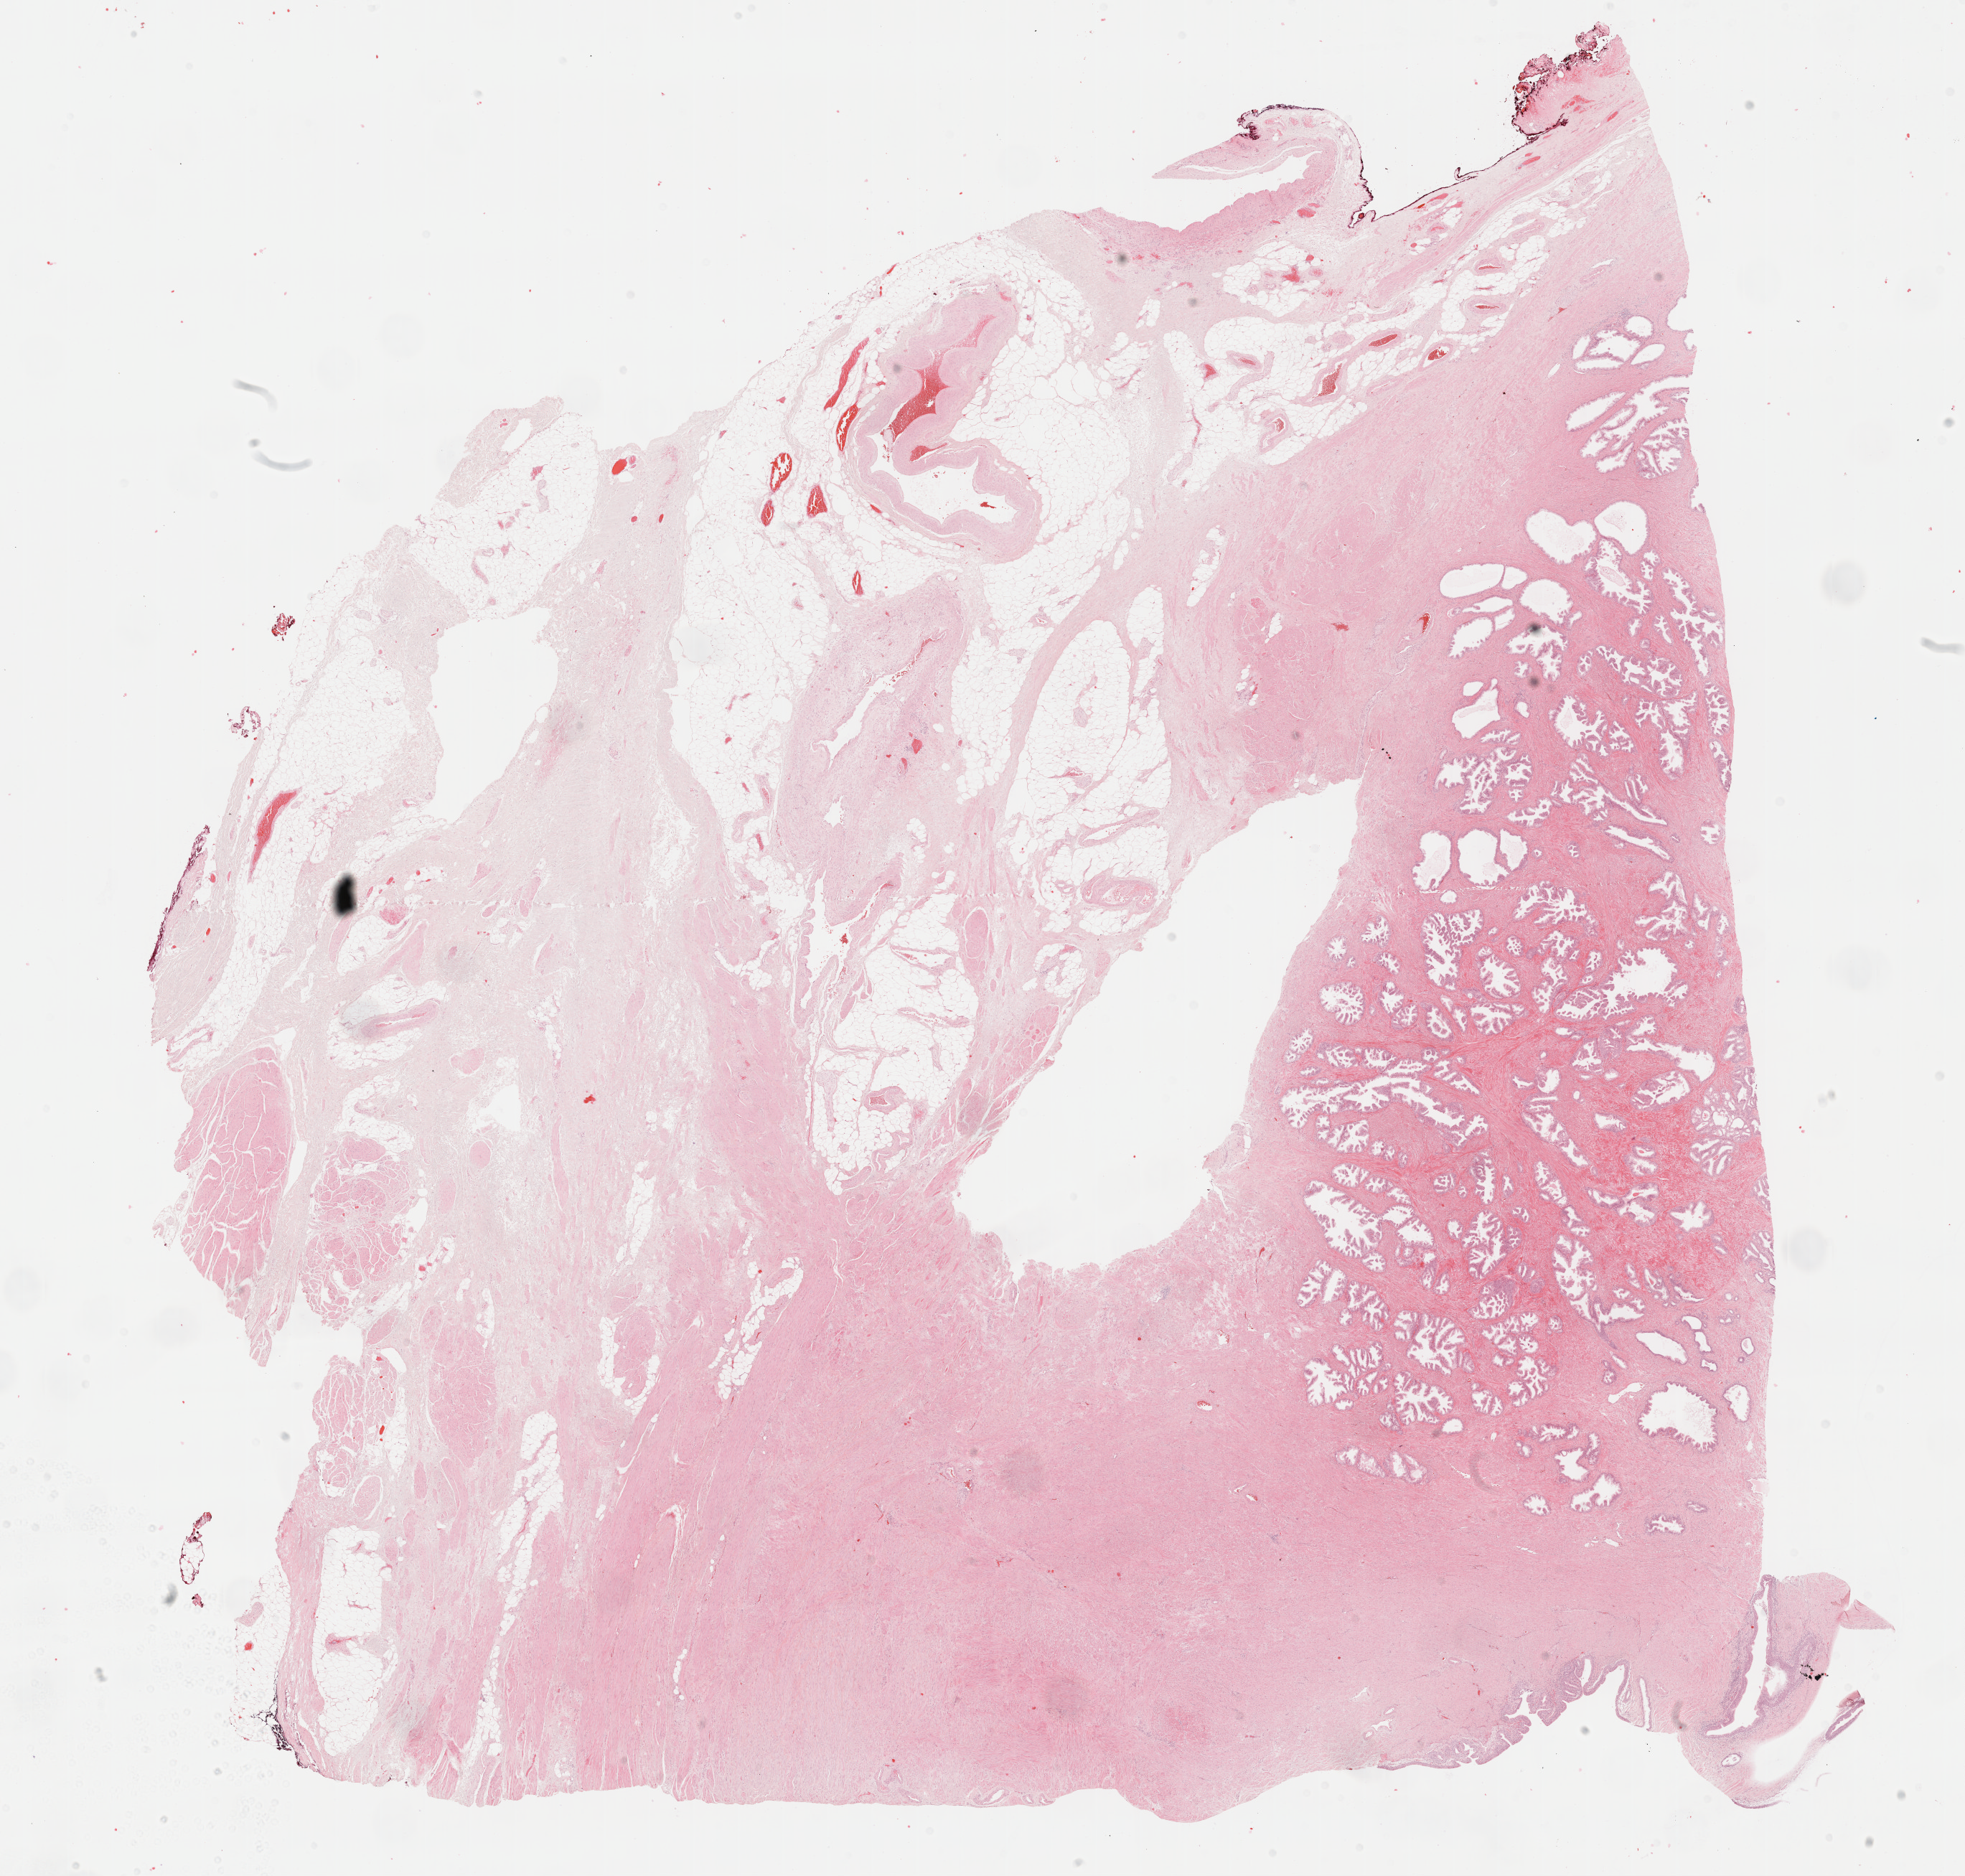
Digitized H&E tissue section (whole slide), a low-resolution overview of the entire scanned area, about 22.1 x 21.1 mm; formalin-fixed paraffin-embedded (FFPE) diagnostic section; primary tumour sample from the prostate. Male patient; age at initial diagnosis 65 years. Gleason score: 6 (3+3).
- histologic diagnosis: Adenocarcinoma, NOS (prostate gland)